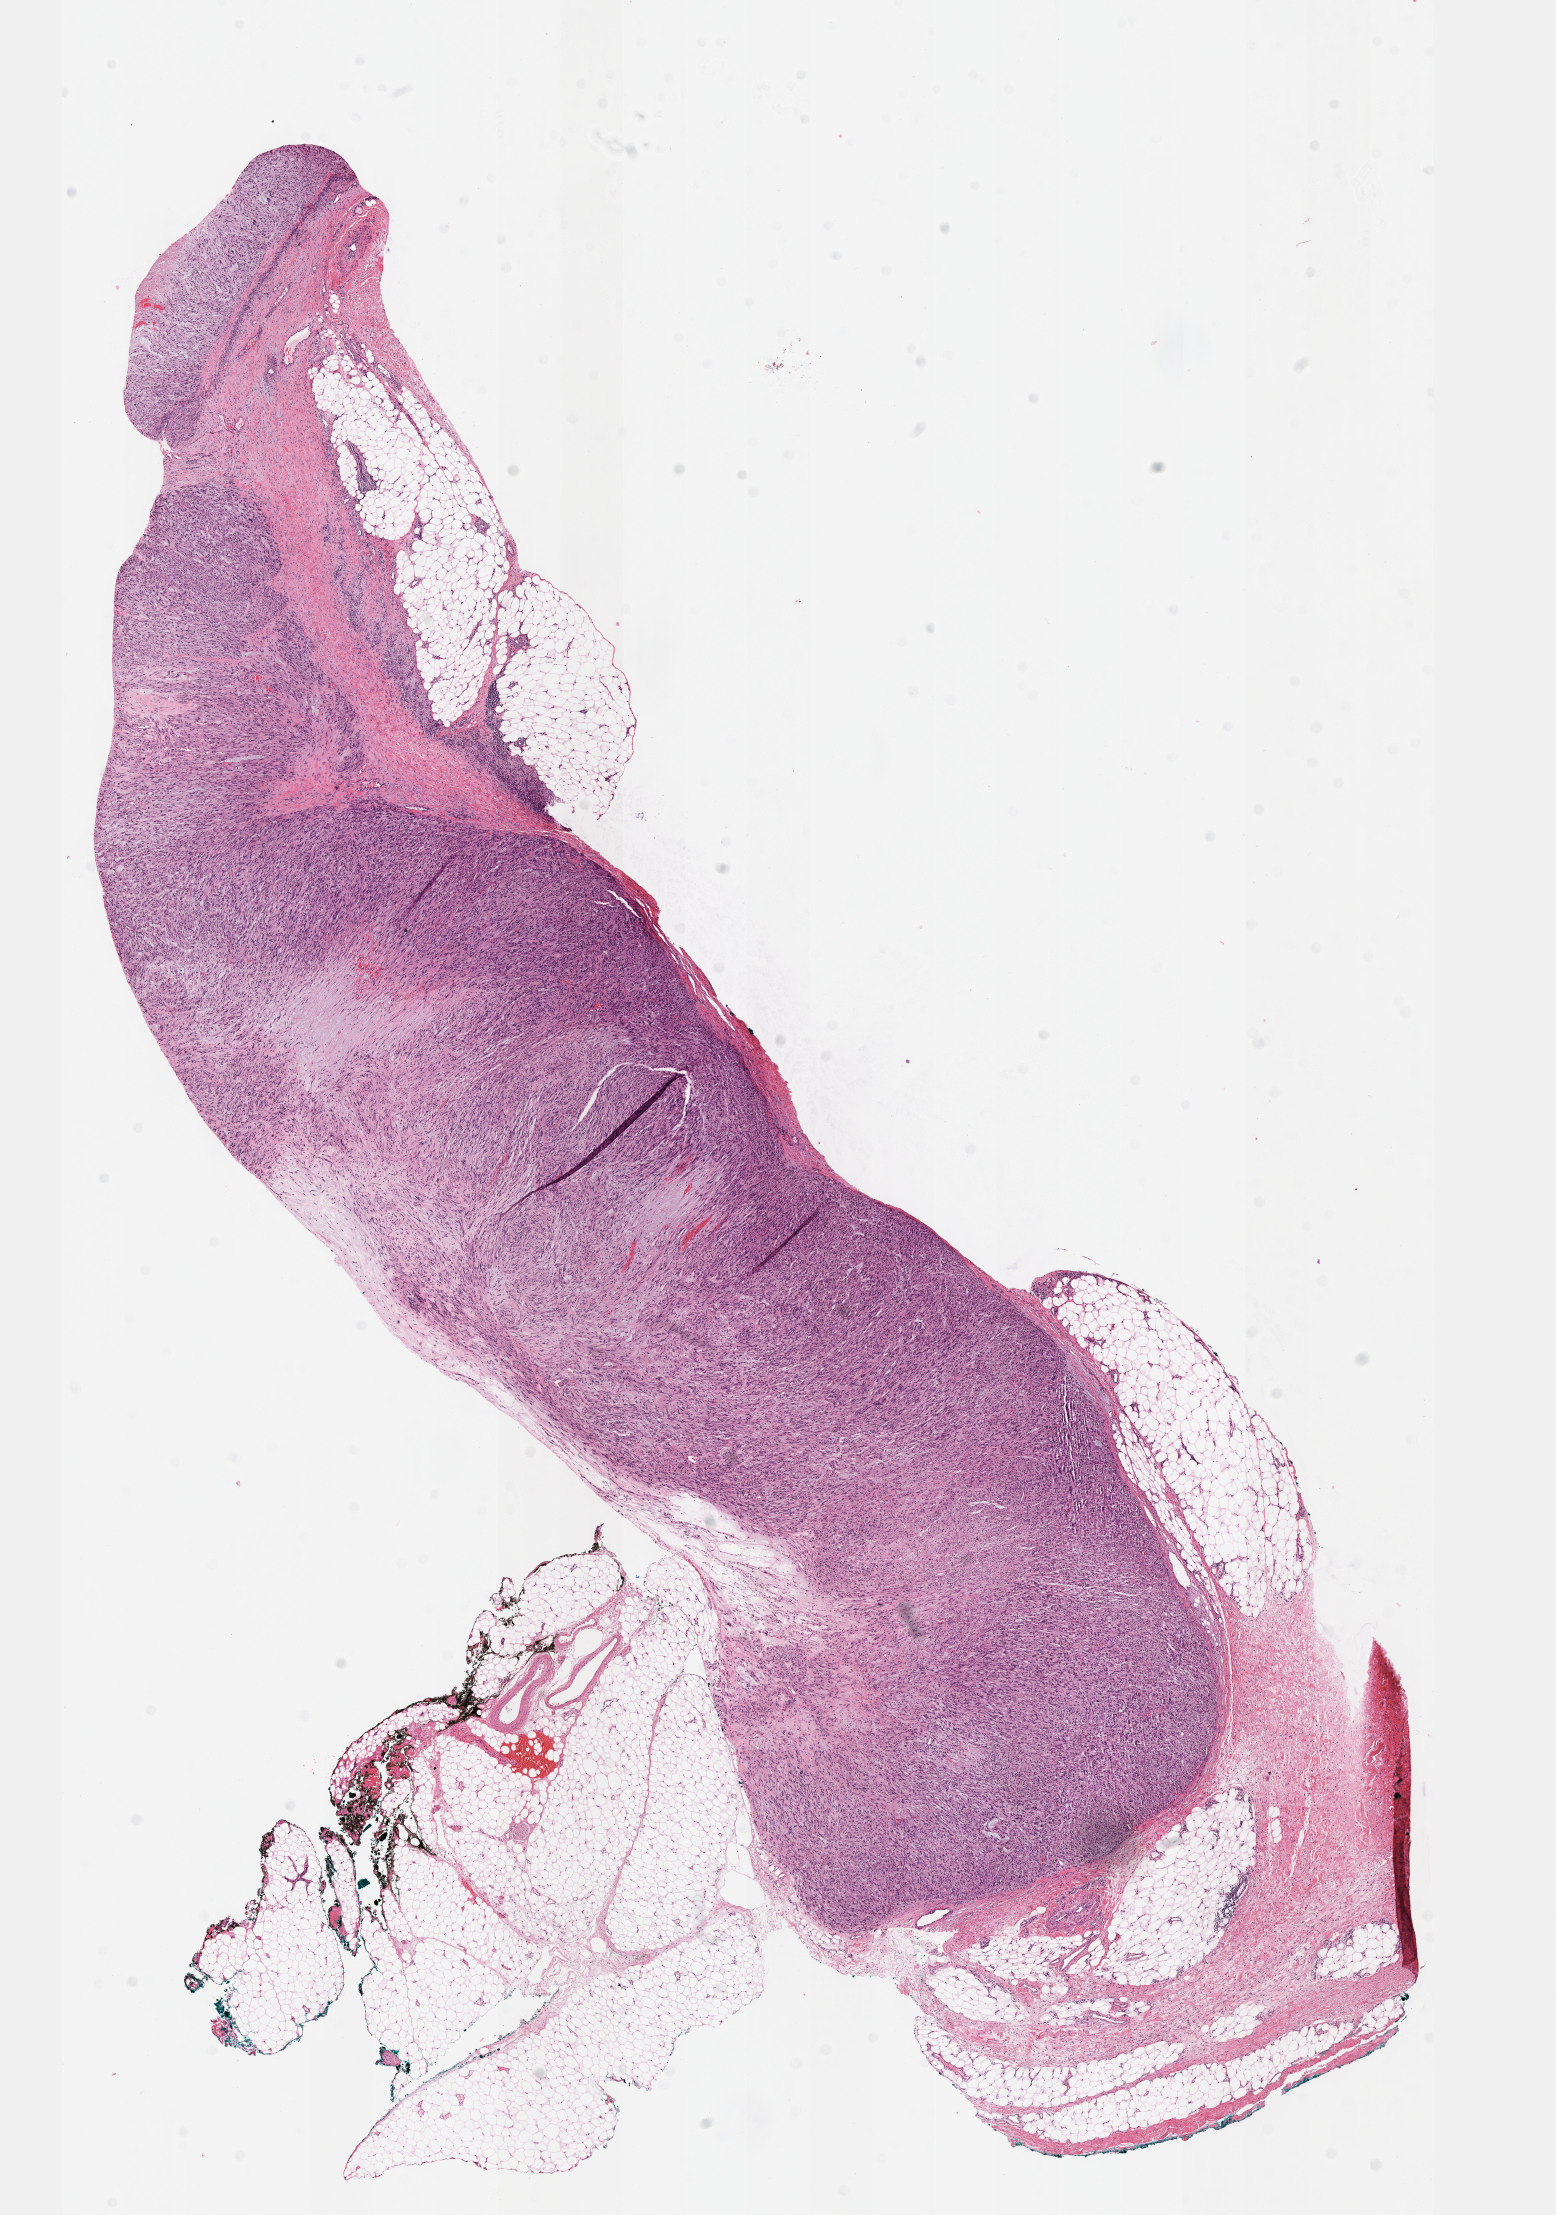
Digitized H&E-stained tissue section (whole slide) — whole scanned area (about 12.6 x 17.9 mm) shown as a low-resolution overview; formalin-fixed paraffin-embedded (FFPE) diagnostic section; primary tumour sample from the connective, subcutaneous and other soft tissues. Female, age 63 years at initial diagnosis.
Histologic diagnosis: Leiomyosarcoma, NOS (connective, subcutaneous and other soft tissues of lower limb and hip).